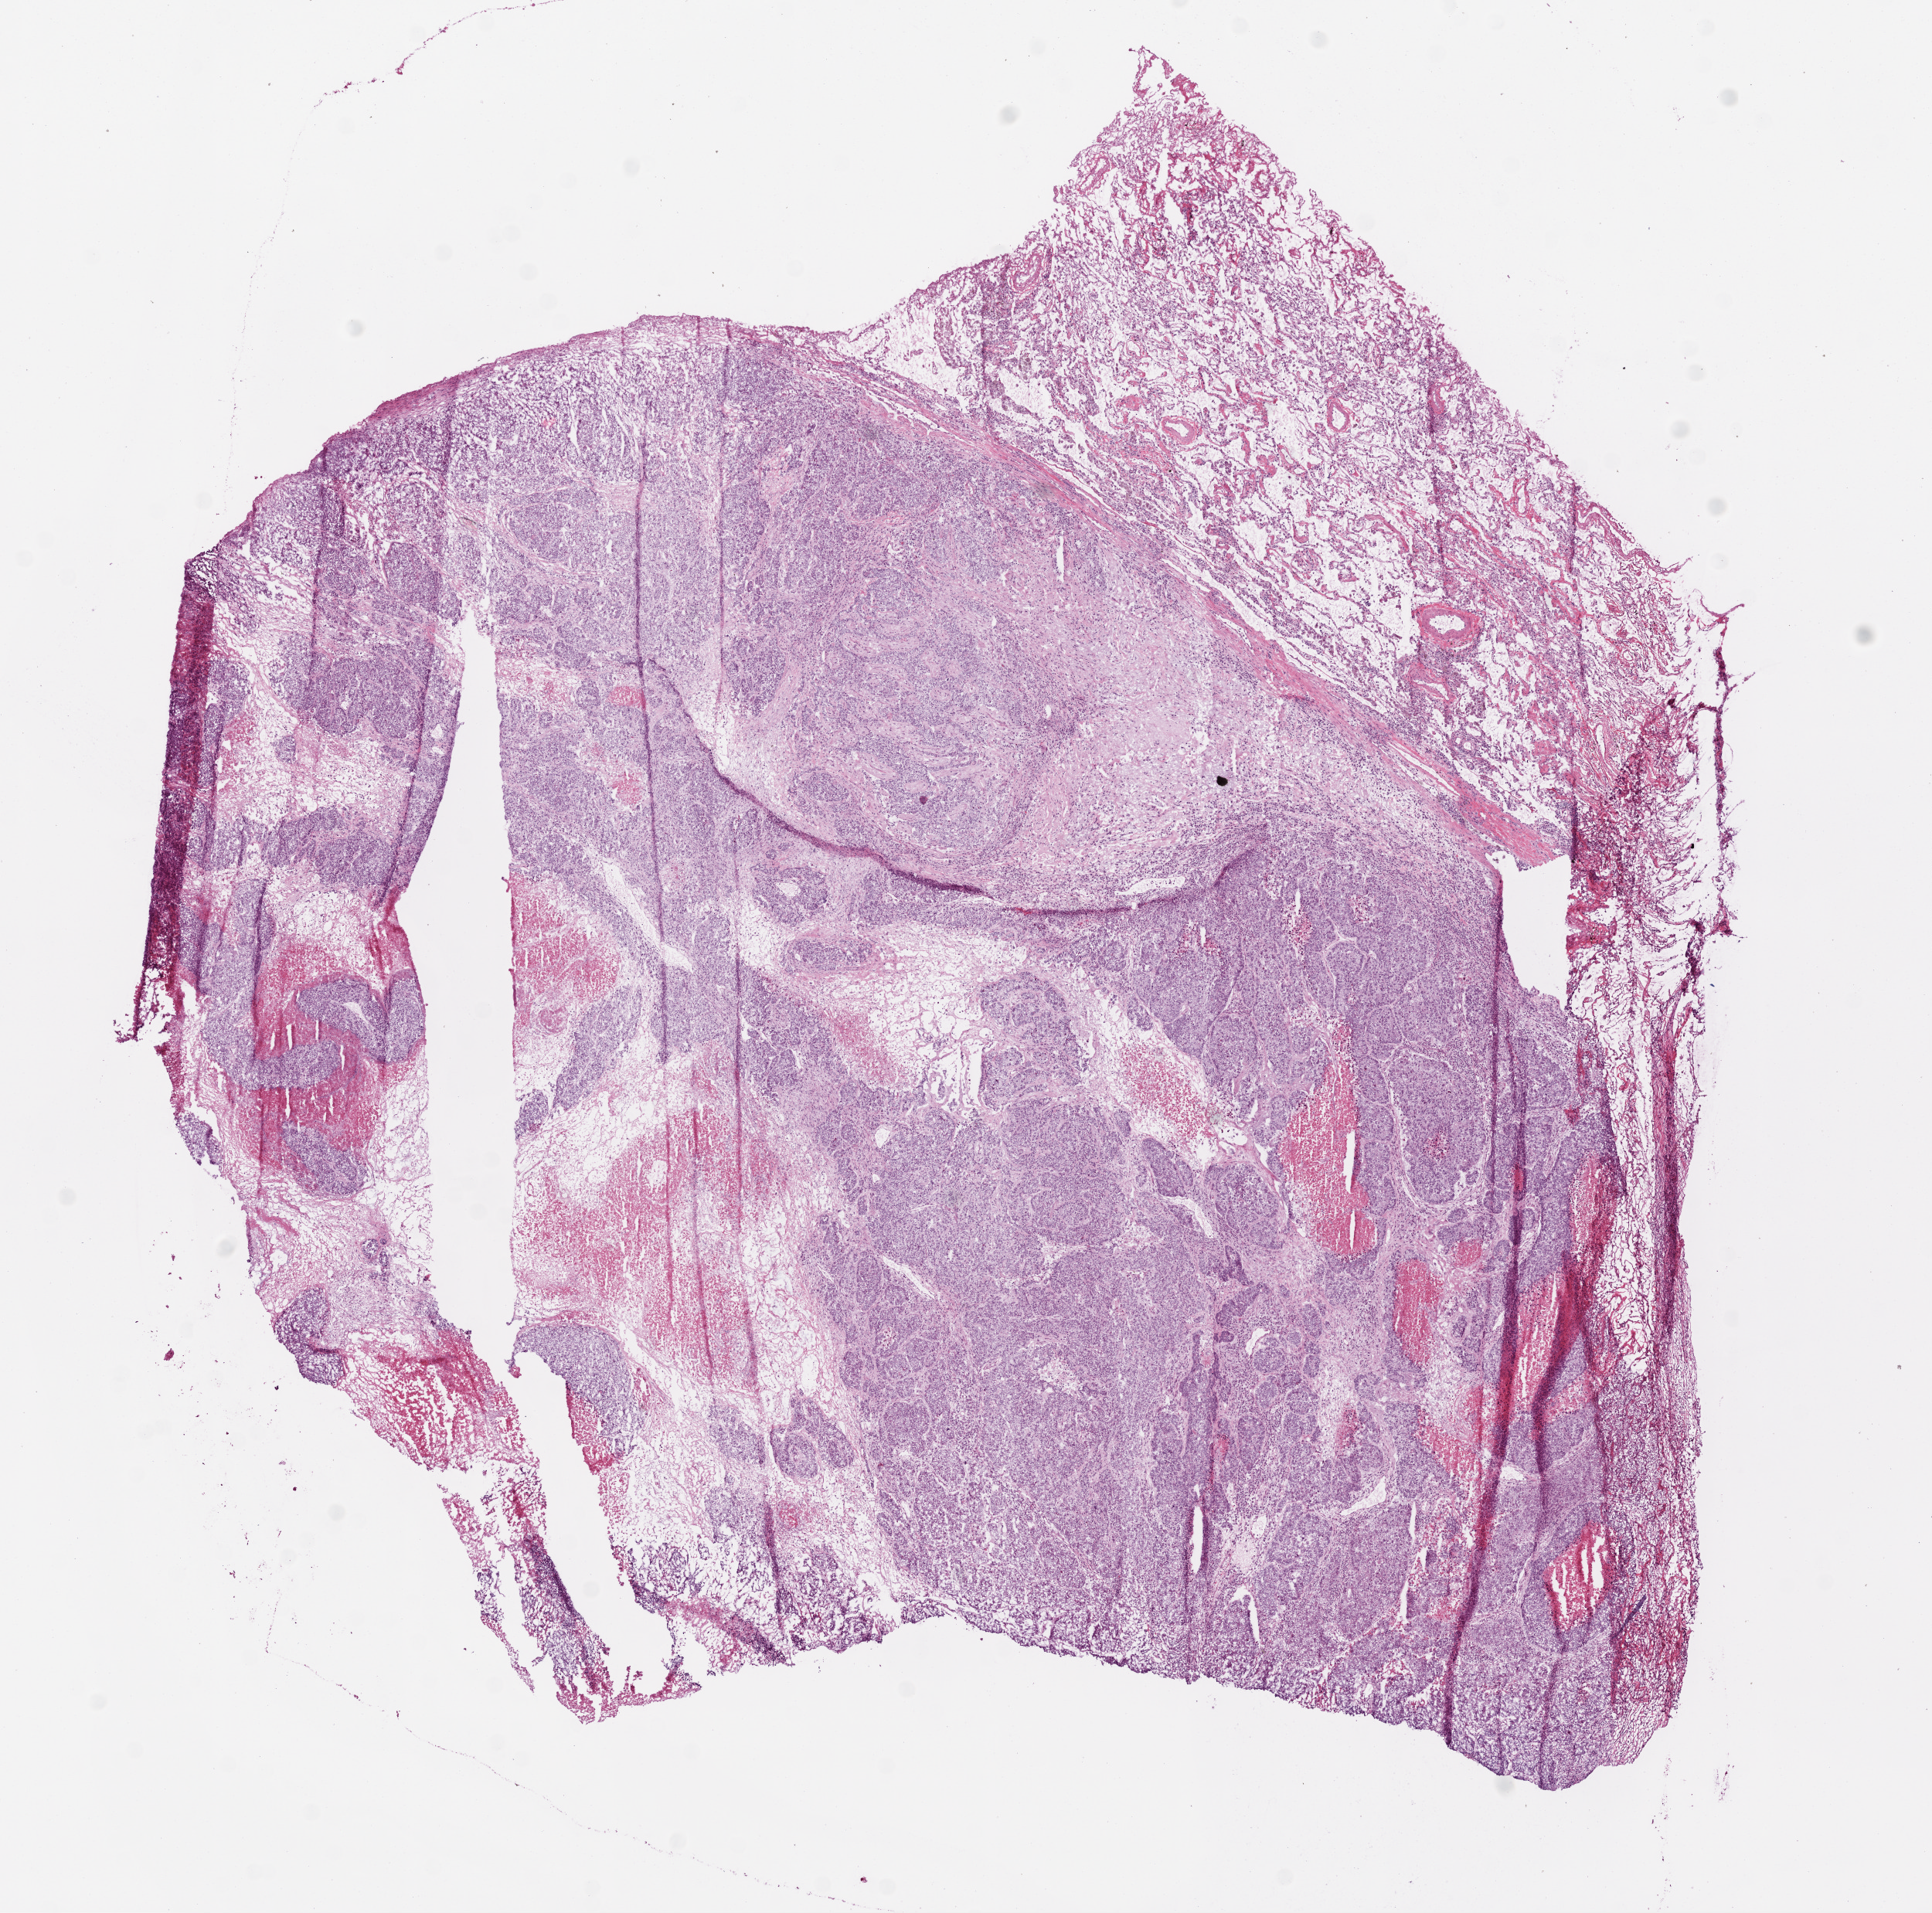
Digitized H&E-stained tissue section (whole slide), a low-resolution overview of the entire scanned area, about 10.0 x 9.9 mm; frozen section from the bottom of the tissue portion; primary tumour sample from the lung. Female, age 61 years at initial diagnosis. Slide review estimates, as recorded: tumour cells 45%, tumour nuclei 75%, normal cells 20%, stromal cells 20%, necrosis 15%.
AJCC pathologic stage: IV. Pathologic diagnosis: Squamous cell carcinoma, NOS (lower lobe, lung).